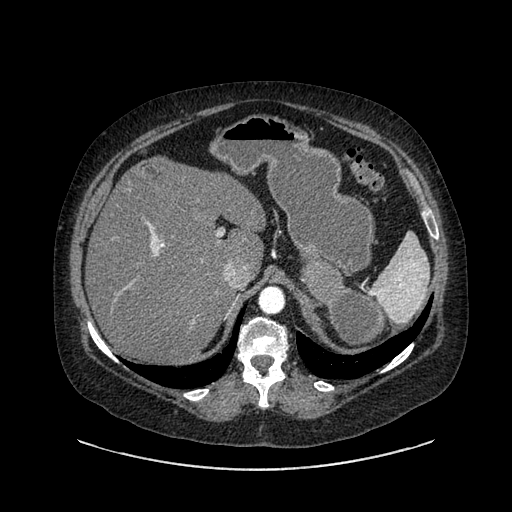
Contrast-enhanced abdominal CT, one axial slice. Position 623 of 769 along the scan axis. Reconstruction kernel SOFT. 120 kVp. Intravenous contrast given. Soft-tissue window (W 400 / L 40 HU). 512 × 512 image matrix, field of view 460 × 460 mm. Female patient, age 61 years. Case-level facts recorded for this patient, not image findings: diagnosis: adrenocortical carcinoma; tumour side: left adrenal; tumour size at pathology: 13 cm.
Annotated regions visible in this slice (semi-automatically segmented with operator editing):
- mass: bounding box [x1, y1, x2, y2] px = [301, 261, 386, 347]